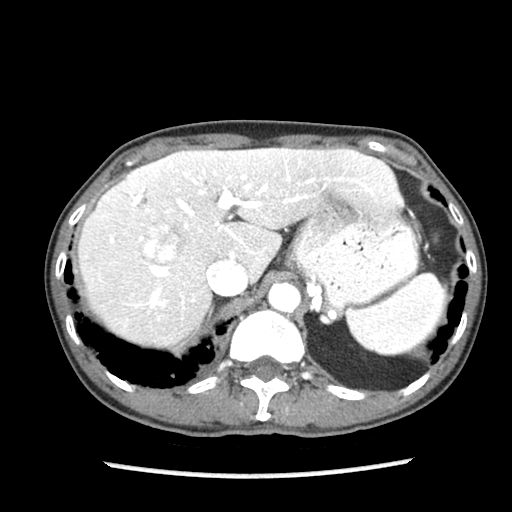
Contrast-enhanced abdominal CT (liver protocol), one axial slice. Reconstruction kernel STANDARD. 140 kVp. Soft-tissue window (W 400 / L 40 HU). 2.5 mm slice thickness. 512 × 512 image matrix, field of view 300 × 300 mm. From the clinical record (not read from this slice): diagnosis: hepatocellular carcinoma (patient treated with transarterial chemoembolisation; whether this scan precedes or follows treatment is not stated here); TNM stage (as recorded): Stage-IIIB; Child-Pugh class: A.
Structures marked on this image (semi-automatic segmentation, software-assisted and operator-edited):
- liver parenchyma outside the tumour (the mass and vessels are separate outlines, so this box may not span the whole liver): bounding box (x1, y1, x2, y2) in pixels: (78, 148, 402, 346)
- mass: (142, 232, 178, 263)
- liver vessels: (110, 160, 372, 306)